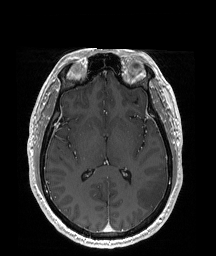
Brain MRI from a brain-tumour surgery series, one axial slice. Slice 98 of 192 in the series (ordered by position). T1-weighted post-contrast. 216 × 256 image matrix, field of view 219 × 260 mm. From the clinical record (not read from this slice): histopathology: Glioblastoma; WHO grade: 4; IDH mutation: no; tumour location: Left Temporal Parietal.
Outlined on this slice (expert manual segmentation):
- tumour: bounding box [x1, y1, x2, y2] px = [138, 172, 168, 209]